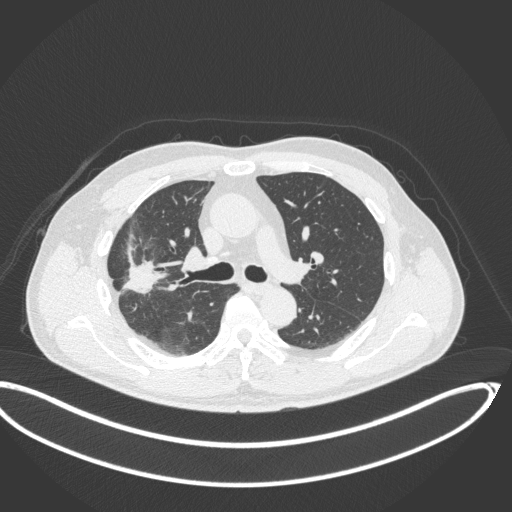
Chest CT, one axial slice; slice 217 of 341 in the series (ordered by position); lung window (W 1500 / L -600 HU); 1 mm slice thickness; 512 × 512 image matrix, field of view 439 × 439 mm. Male patient, age 63 years. From the clinical record (not read from this slice): clinical TNM (as recorded): T1c N0 M0; histopathological grade: G2-3.
Annotated regions visible in this slice (bounding box drawn by a radiologist):
- lung tumour (recorded histology: adenocarcinoma): bounding box [x1, y1, x2, y2] px = [123, 258, 160, 298]